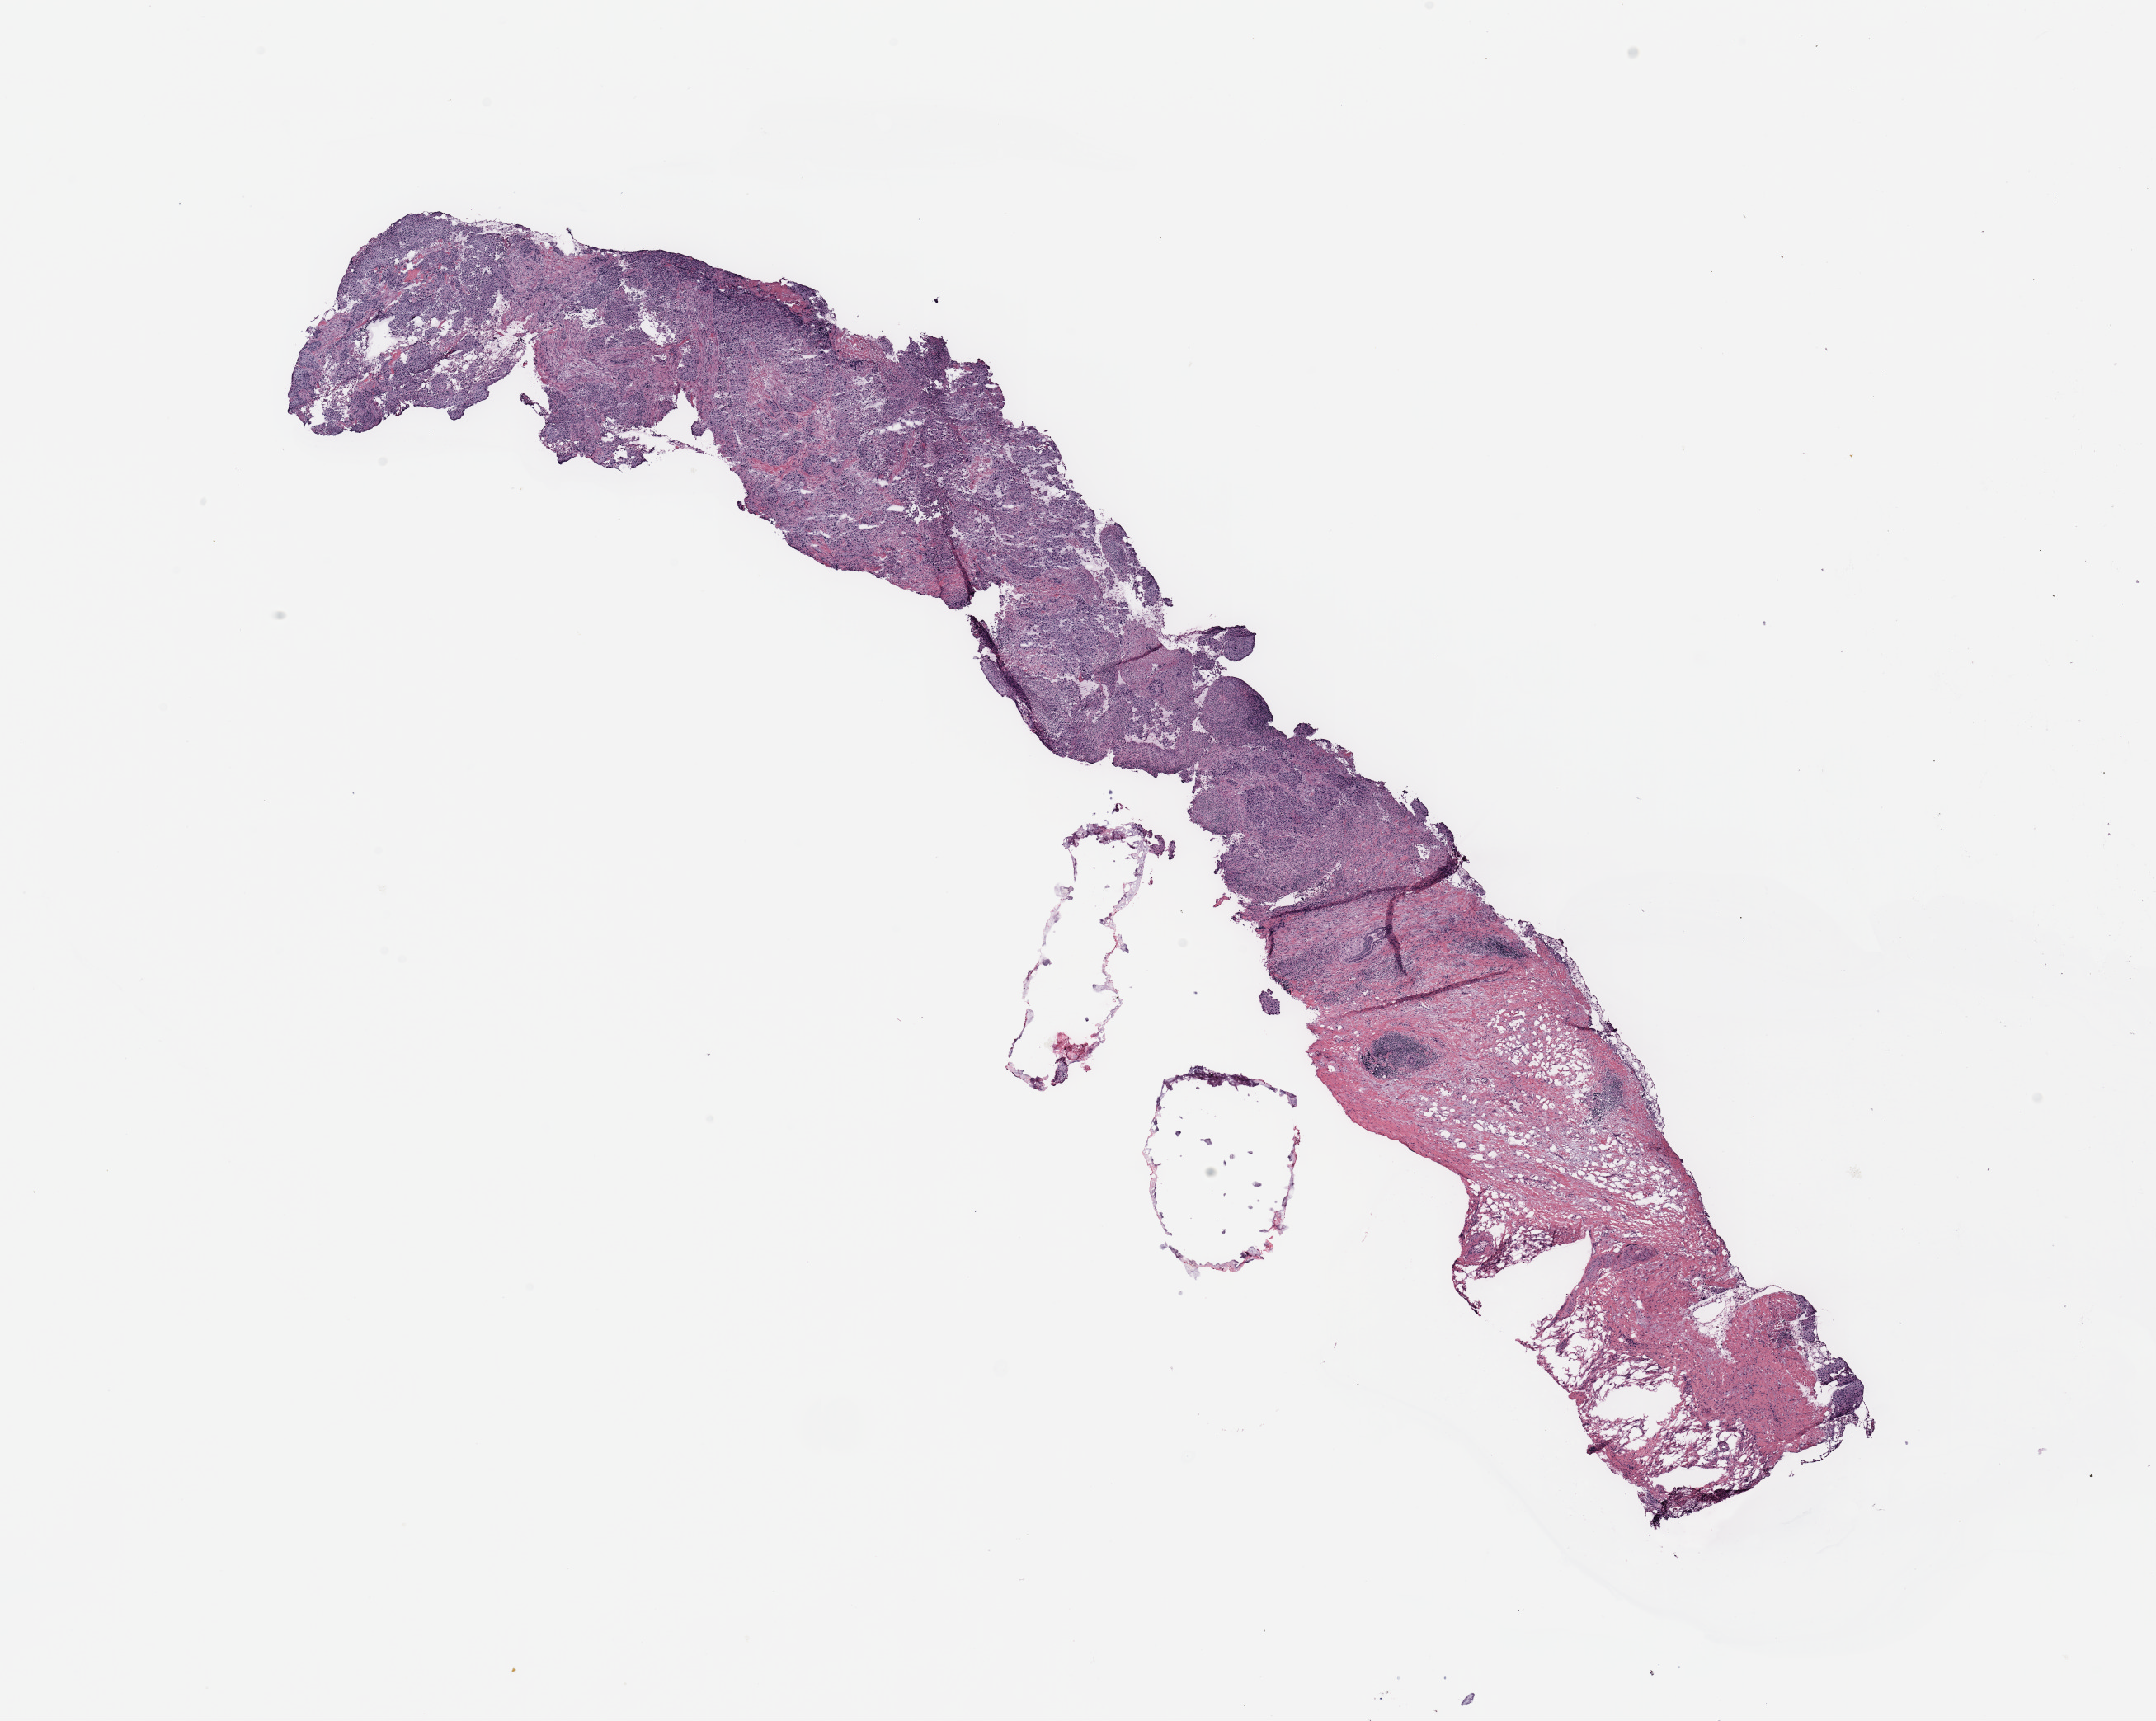
Whole-slide histology image, H&E, shown as a low-resolution overview of the whole scanned area (about 20.7 x 16.5 mm), breast, tumour tissue. Patient: female, age 61 years.
Diagnosis: Infiltrating duct carcinoma, NOS. AJCC pathologic stage: III.